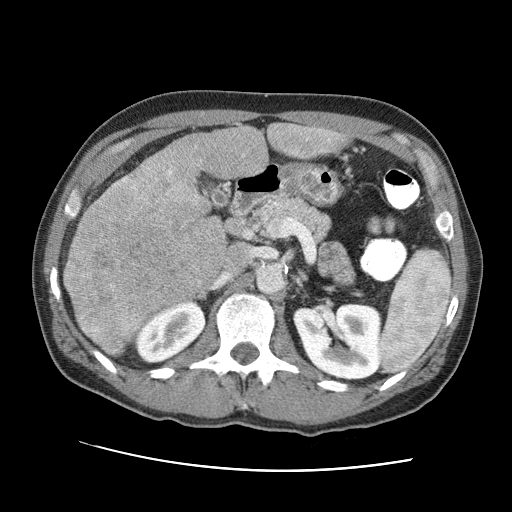
Contrast-enhanced abdominal CT (liver protocol), one axial slice; slice 38 of 95 in the series (ordered by position); 120 kVp; one of 2 acquisitions stored at this slice position; soft-tissue window (W 400 / L 40 HU); 512 × 512 image matrix, field of view 360 × 360 mm. From the clinical record (not read from this slice): diagnosis: hepatocellular carcinoma (patient treated with transarterial chemoembolisation; whether this scan precedes or follows treatment is not stated here); TNM stage (as recorded): Stage-IVA; Child-Pugh class: A; tumour differentiation: moderately differentiated.
Structures marked on this image (semi-automatic segmentation, software-assisted and operator-edited):
- liver parenchyma outside the tumour (the mass and vessels are separate outlines, so this box may not span the whole liver): bounding box (x1, y1, x2, y2) in pixels: (62, 122, 346, 354)
- mass: (63, 153, 227, 355)
- liver vessels: (195, 125, 336, 166)